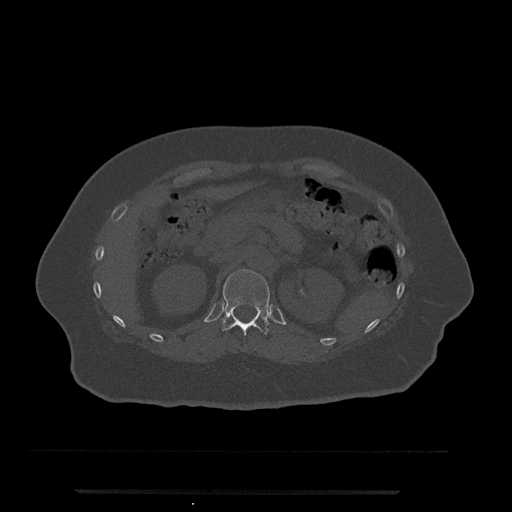
CT including the spine, one axial slice; position 169 of 797 along the scan axis; reconstruction kernel Br40s/3; bone window (W 1800 / L 400 HU); 0.5 mm slice thickness; 512 × 512 image matrix, field of view 440 × 440 mm. Female patient, age 51 years. Case-level facts recorded for this patient, not image findings: primary cancer: neuro.
Structures marked on this image (semi-automatically segmented with operator editing):
- T12 vertebra: box from (x=221, y=269) to (x=270, y=335) px